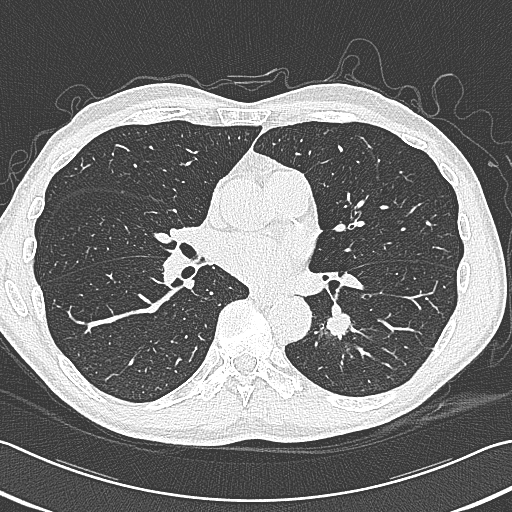
Low-dose screening chest CT, axial slice; baseline screening round; lung window (W 1500 / L -600 HU); 1 mm slice thickness; lung (sharp) reconstruction kernel (B80f); slice 179 of 354 in the series; 512 × 512 image matrix. Male participant, aged 59 years at enrolment. Former smoker at enrolment.
Expert reader's lesion annotation, bounding box <312,295,376,353> (left, top, right, bottom; pixels). Screening reader's record for this exam (one nodule recorded; not confirmed to be the boxed lesion): non-calcified nodule or mass ≥4 mm, left lower lobe, 15 × 15 mm, smooth margins, soft tissue attenuation. Participant outcome: lung cancer diagnosed 17 days after this screen — squamous cell carcinoma, large cell, nonkeratinizing, NOS, left lower lobe, poorly differentiated (G3), stage IB (AJCC 6th edition), 31 mm at pathology.